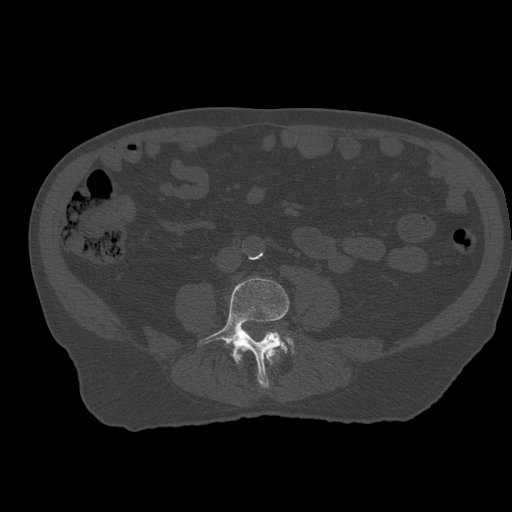
CT including the spine, one axial slice; slice 165 of 399 in the series (ordered by position); reconstruction kernel STANDARD; 120 kVp; bone window (W 1800 / L 400 HU); 1.25 mm slice thickness; 512 × 512 image matrix. Patient age 73 years. Case-level facts recorded for this patient, not image findings: primary cancer: prostate; vertebrae with lytic lesions (as recorded): L2.
Annotated regions visible in this slice (semi-automatic segmentation, software-assisted and operator-edited):
- L3 vertebra: bounding box (x1, y1, x2, y2) in pixels: (236, 347, 280, 363)
- L4 vertebra: (198, 278, 293, 388)
- L5 vertebra: (288, 340, 294, 353)